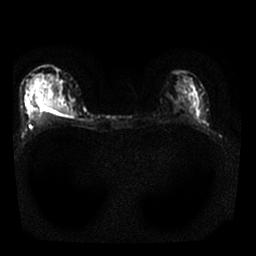
Breast MRI, one axial slice; diffusion-weighted series; image 2 of 4 stored at this slice position (different b-values; order by instance number); 1.5 T; 4 mm slice thickness; 256 × 256 image matrix, field of view 310 × 310 mm. Female patient.
Annotated regions visible in this slice (expert manual segmentation):
- tumour on diffusion-weighted imaging: bounding box (x1, y1, x2, y2) in pixels: (38, 98, 74, 115)